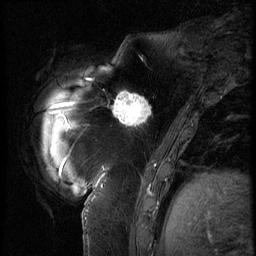
Breast MRI (dynamic contrast-enhanced), one sagittal slice. Slice 16 of 62 in the series (ordered by position). 3 images stored at this slice position (order not interpretable as contrast timing). 1.5 T. TE 4.2 ms, TR 9 ms. 2.5 mm slice thickness. 256 × 256 image matrix, field of view 180 × 180 mm. Patient: female, 57 years. From the clinical record (not read from this slice): setting: breast cancer imaged before/during neoadjuvant chemotherapy; receptor status: triple-negative.
Annotated regions visible in this slice (semi-automatically segmented with operator editing):
- analysis volume of interest (the breast-tissue region the enhancement analysis was run in; not a lesion): box from (x=105, y=84) to (x=158, y=135) px
- tumour enhancement mask (voxels above the 140 % enhancement threshold inside the analysis volume of interest): (x=112, y=90)–(x=151, y=127)